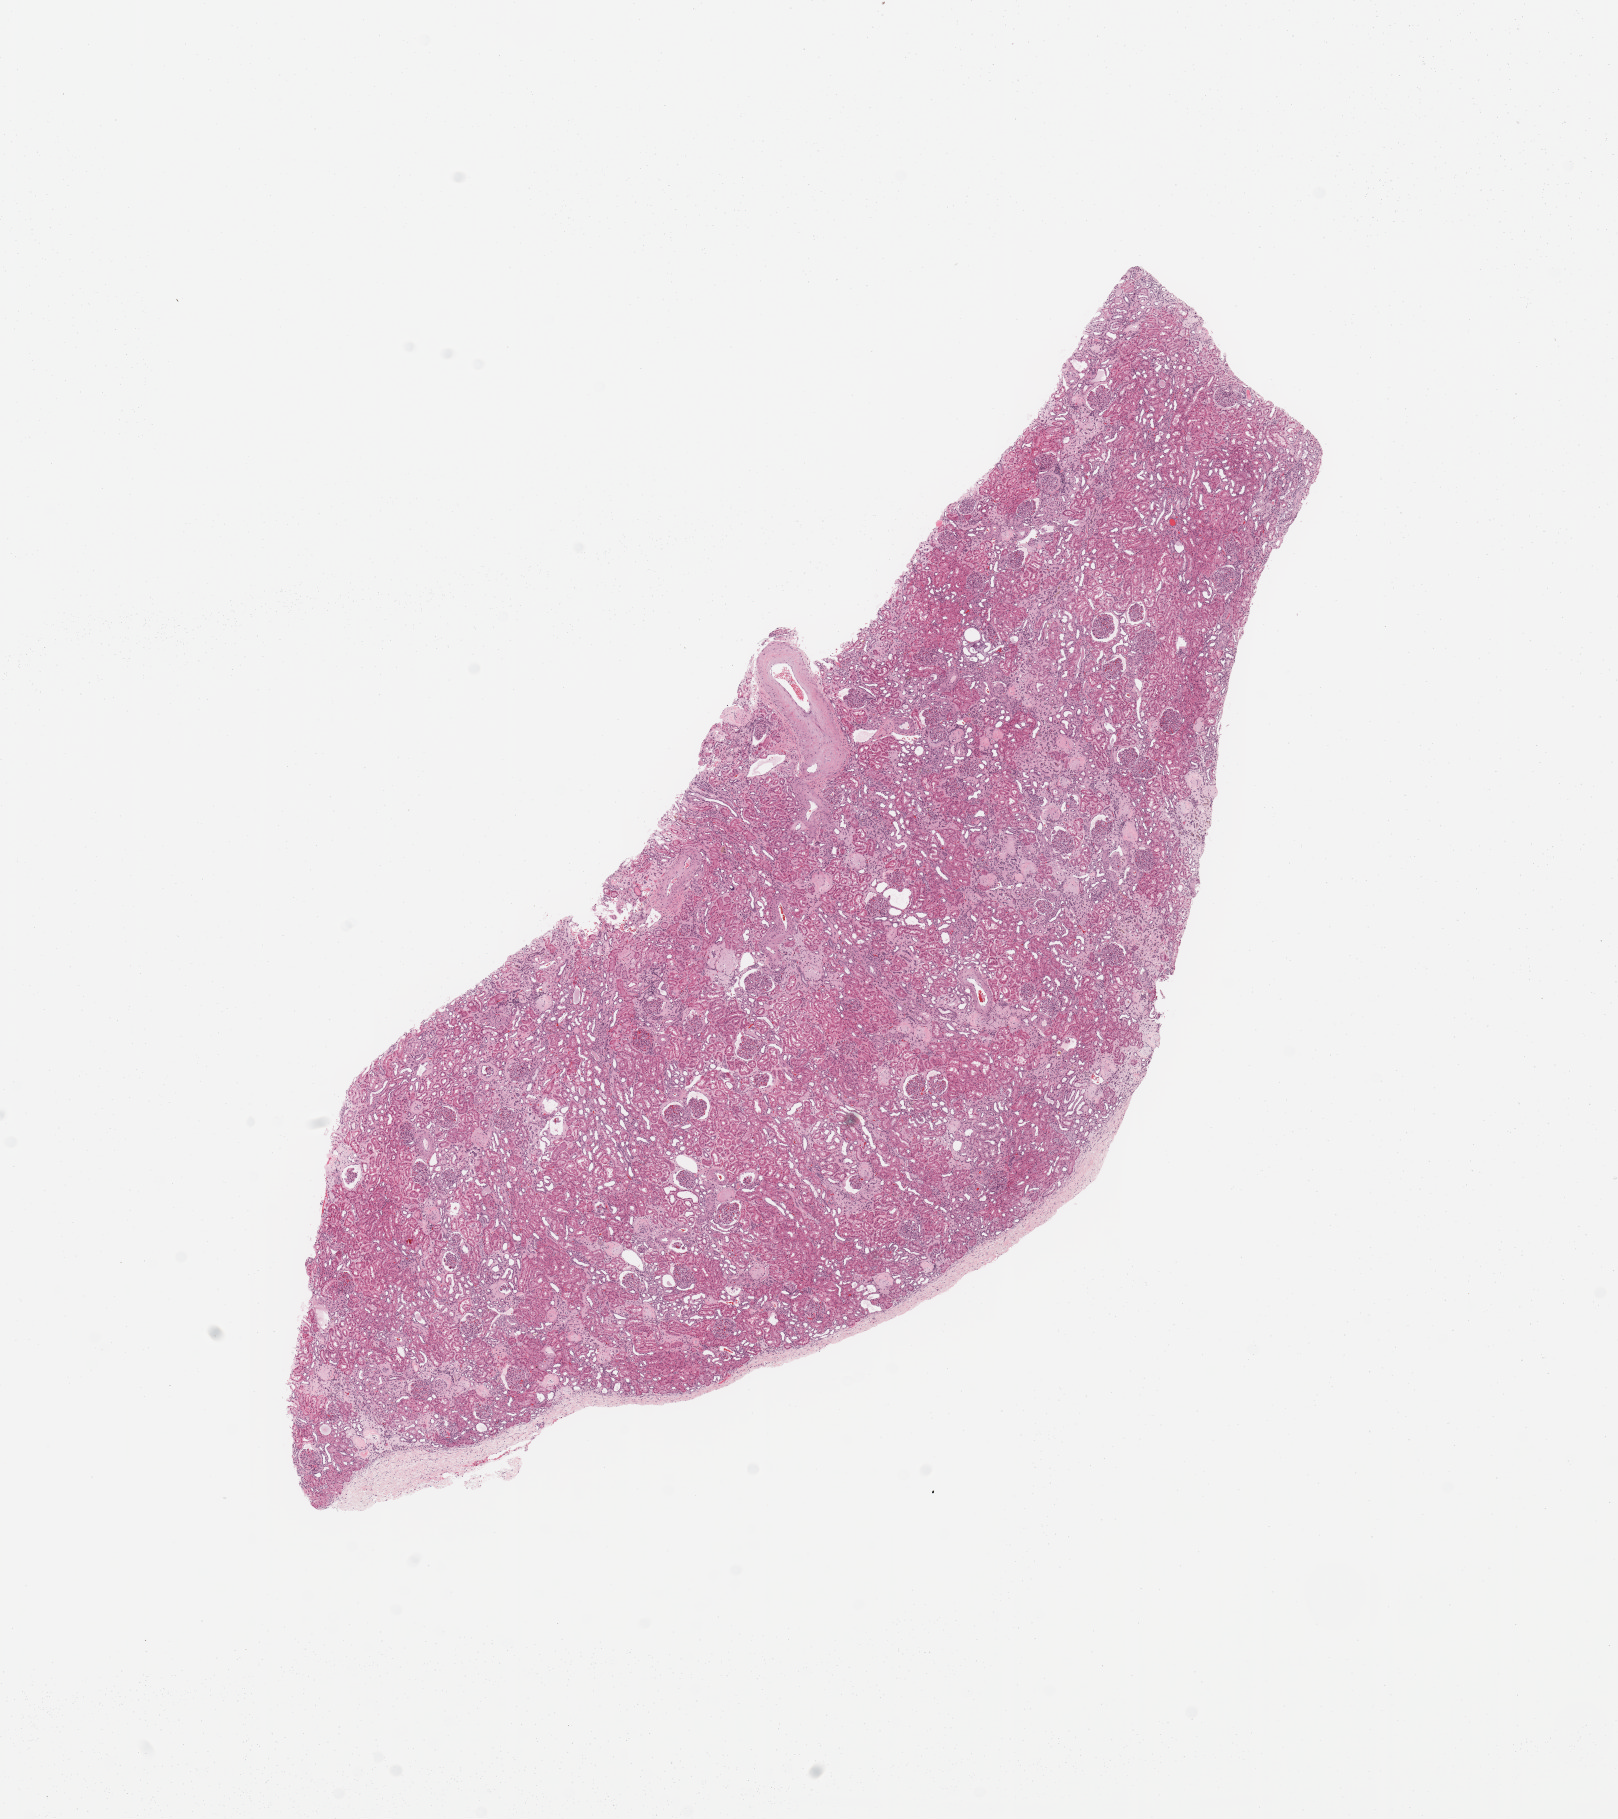
Whole-slide histology image, Hematoxylin and eosin (H&E) stained, a low-resolution overview of the entire scanned area, about 12.8 x 14.4 mm, normal (non-tumour) tissue sample, sampled site: kidney. 68-year-old female patient.
This section: normal (non-tumour) tissue from the same patient. Patient diagnosis: Renal cell carcinoma, NOS.